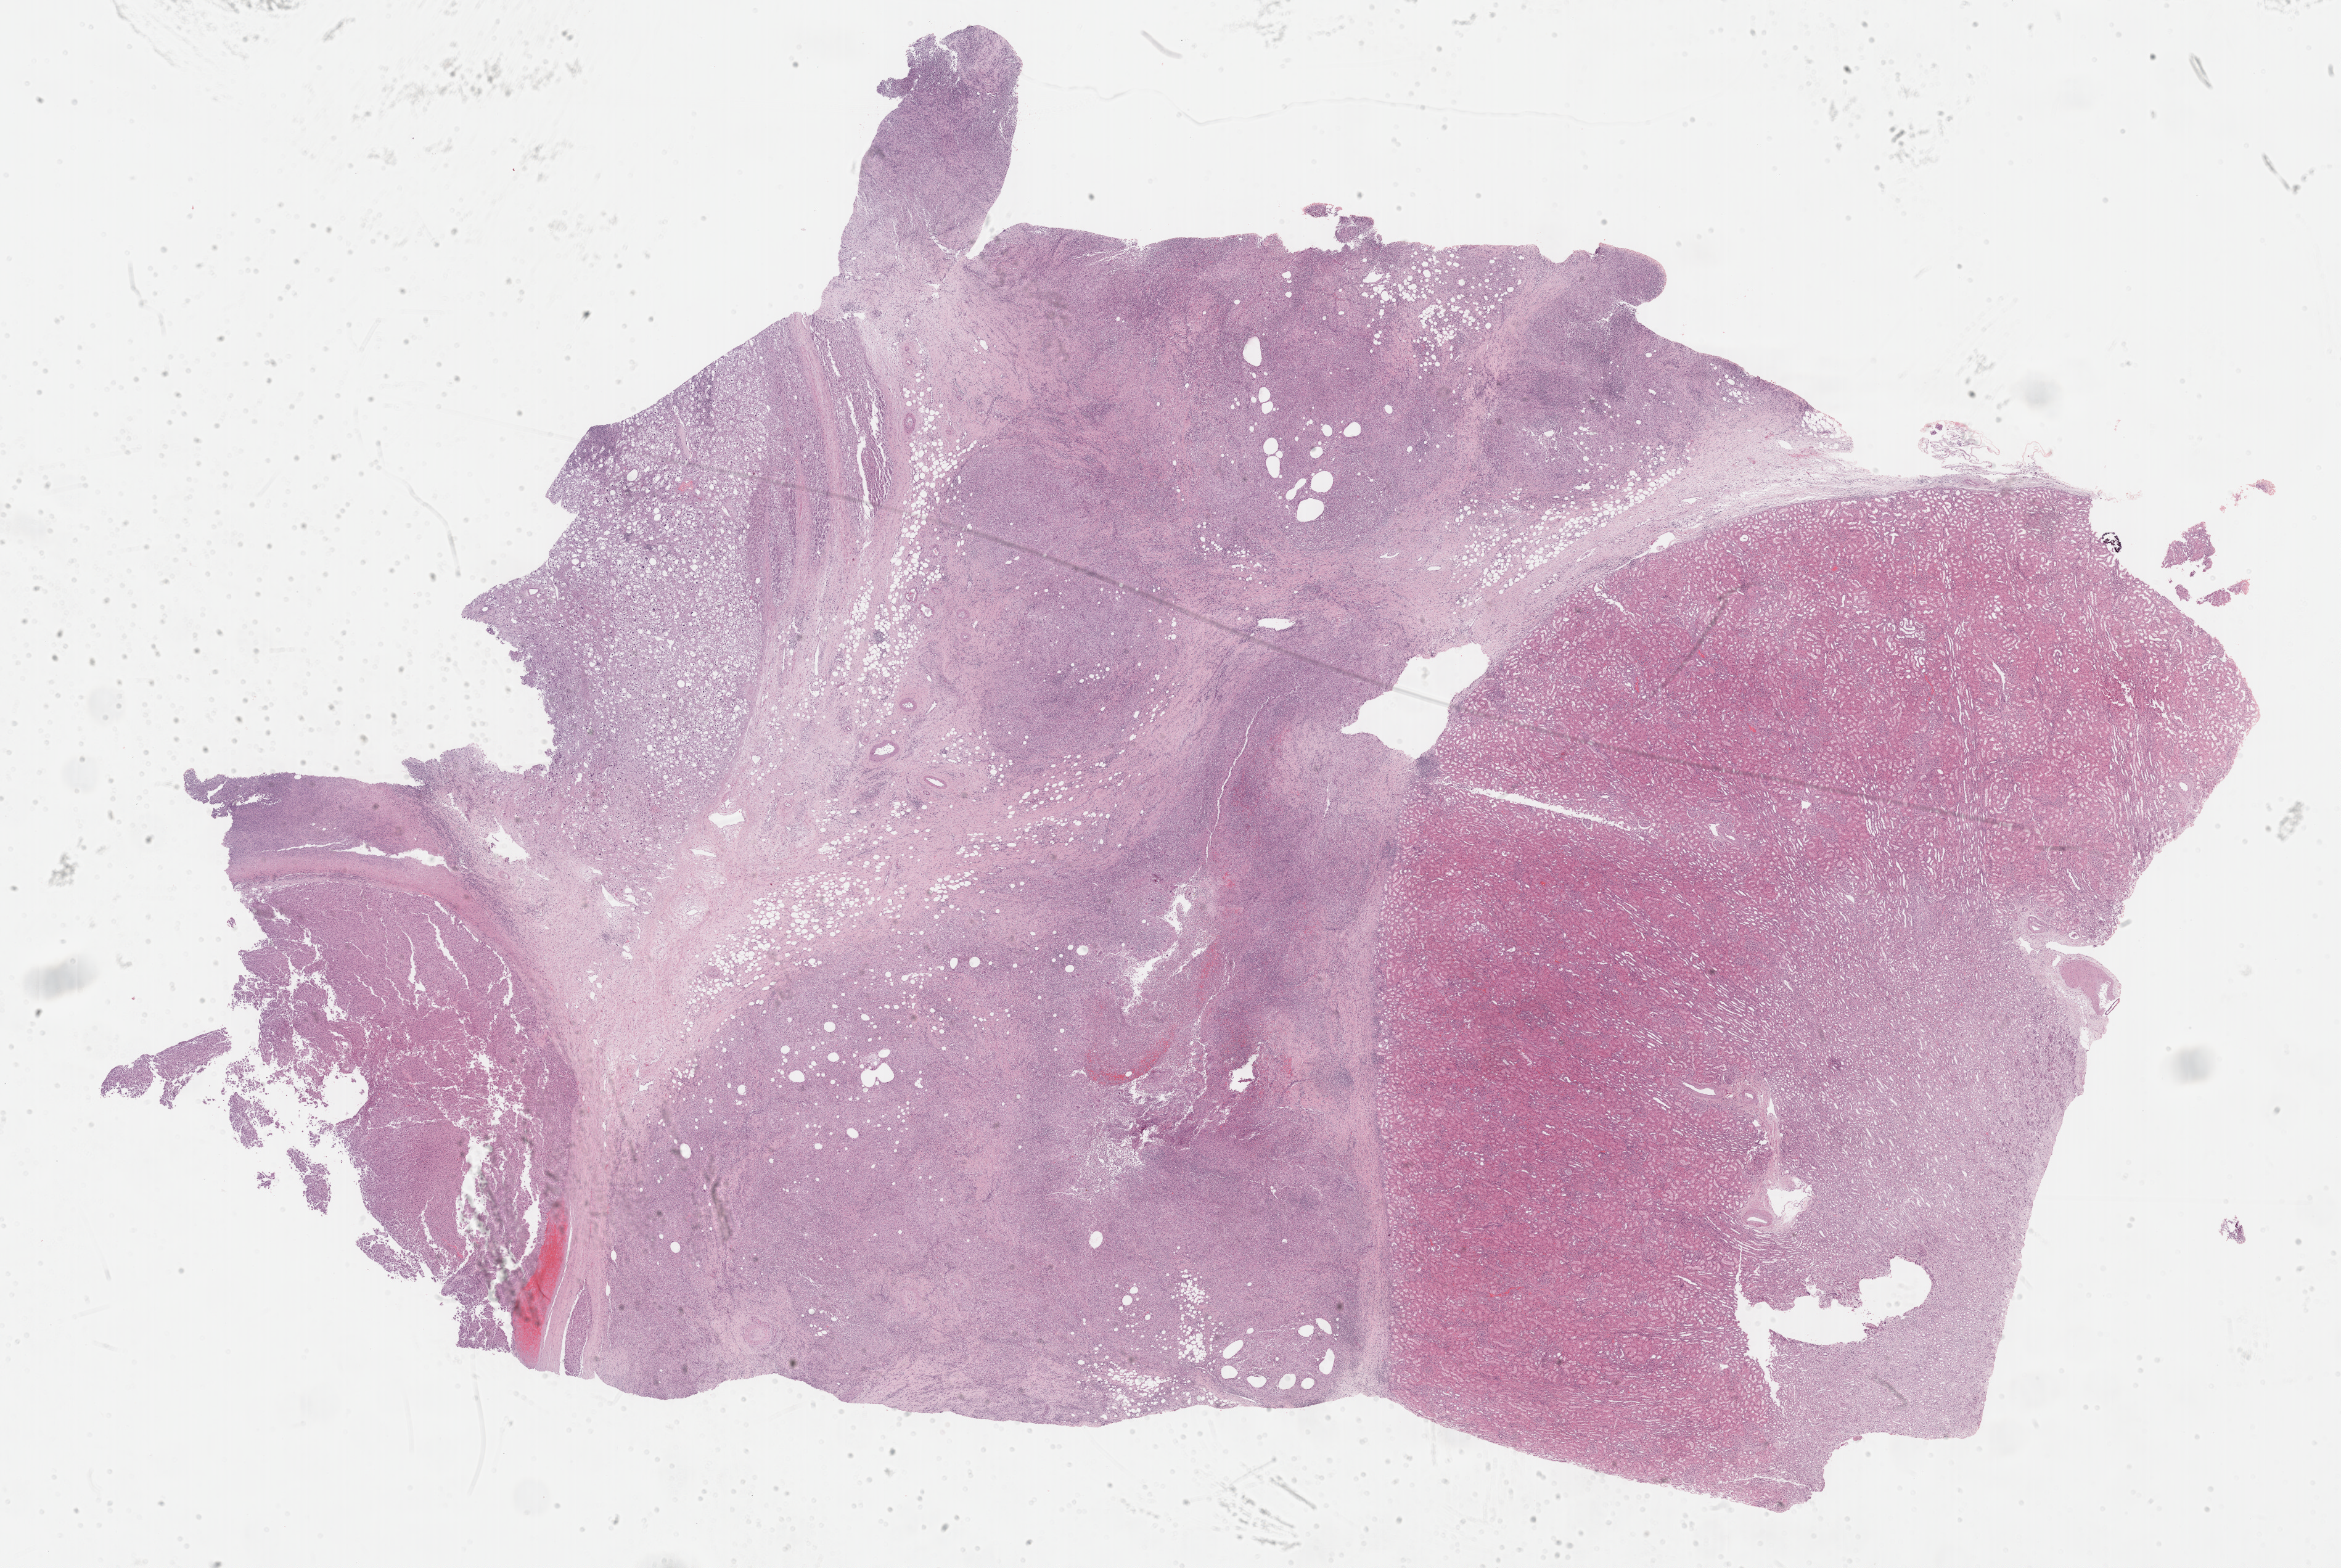
Digitized H&E-stained tissue section (whole slide), low-resolution overview of the scanned area, about 30.7 x 20.6 mm; formalin-fixed paraffin-embedded (FFPE) diagnostic section; sample: primary tumour, adrenal cortex. Female patient; age at initial diagnosis 65 years.
• histologic diagnosis: Adrenal cortical carcinoma